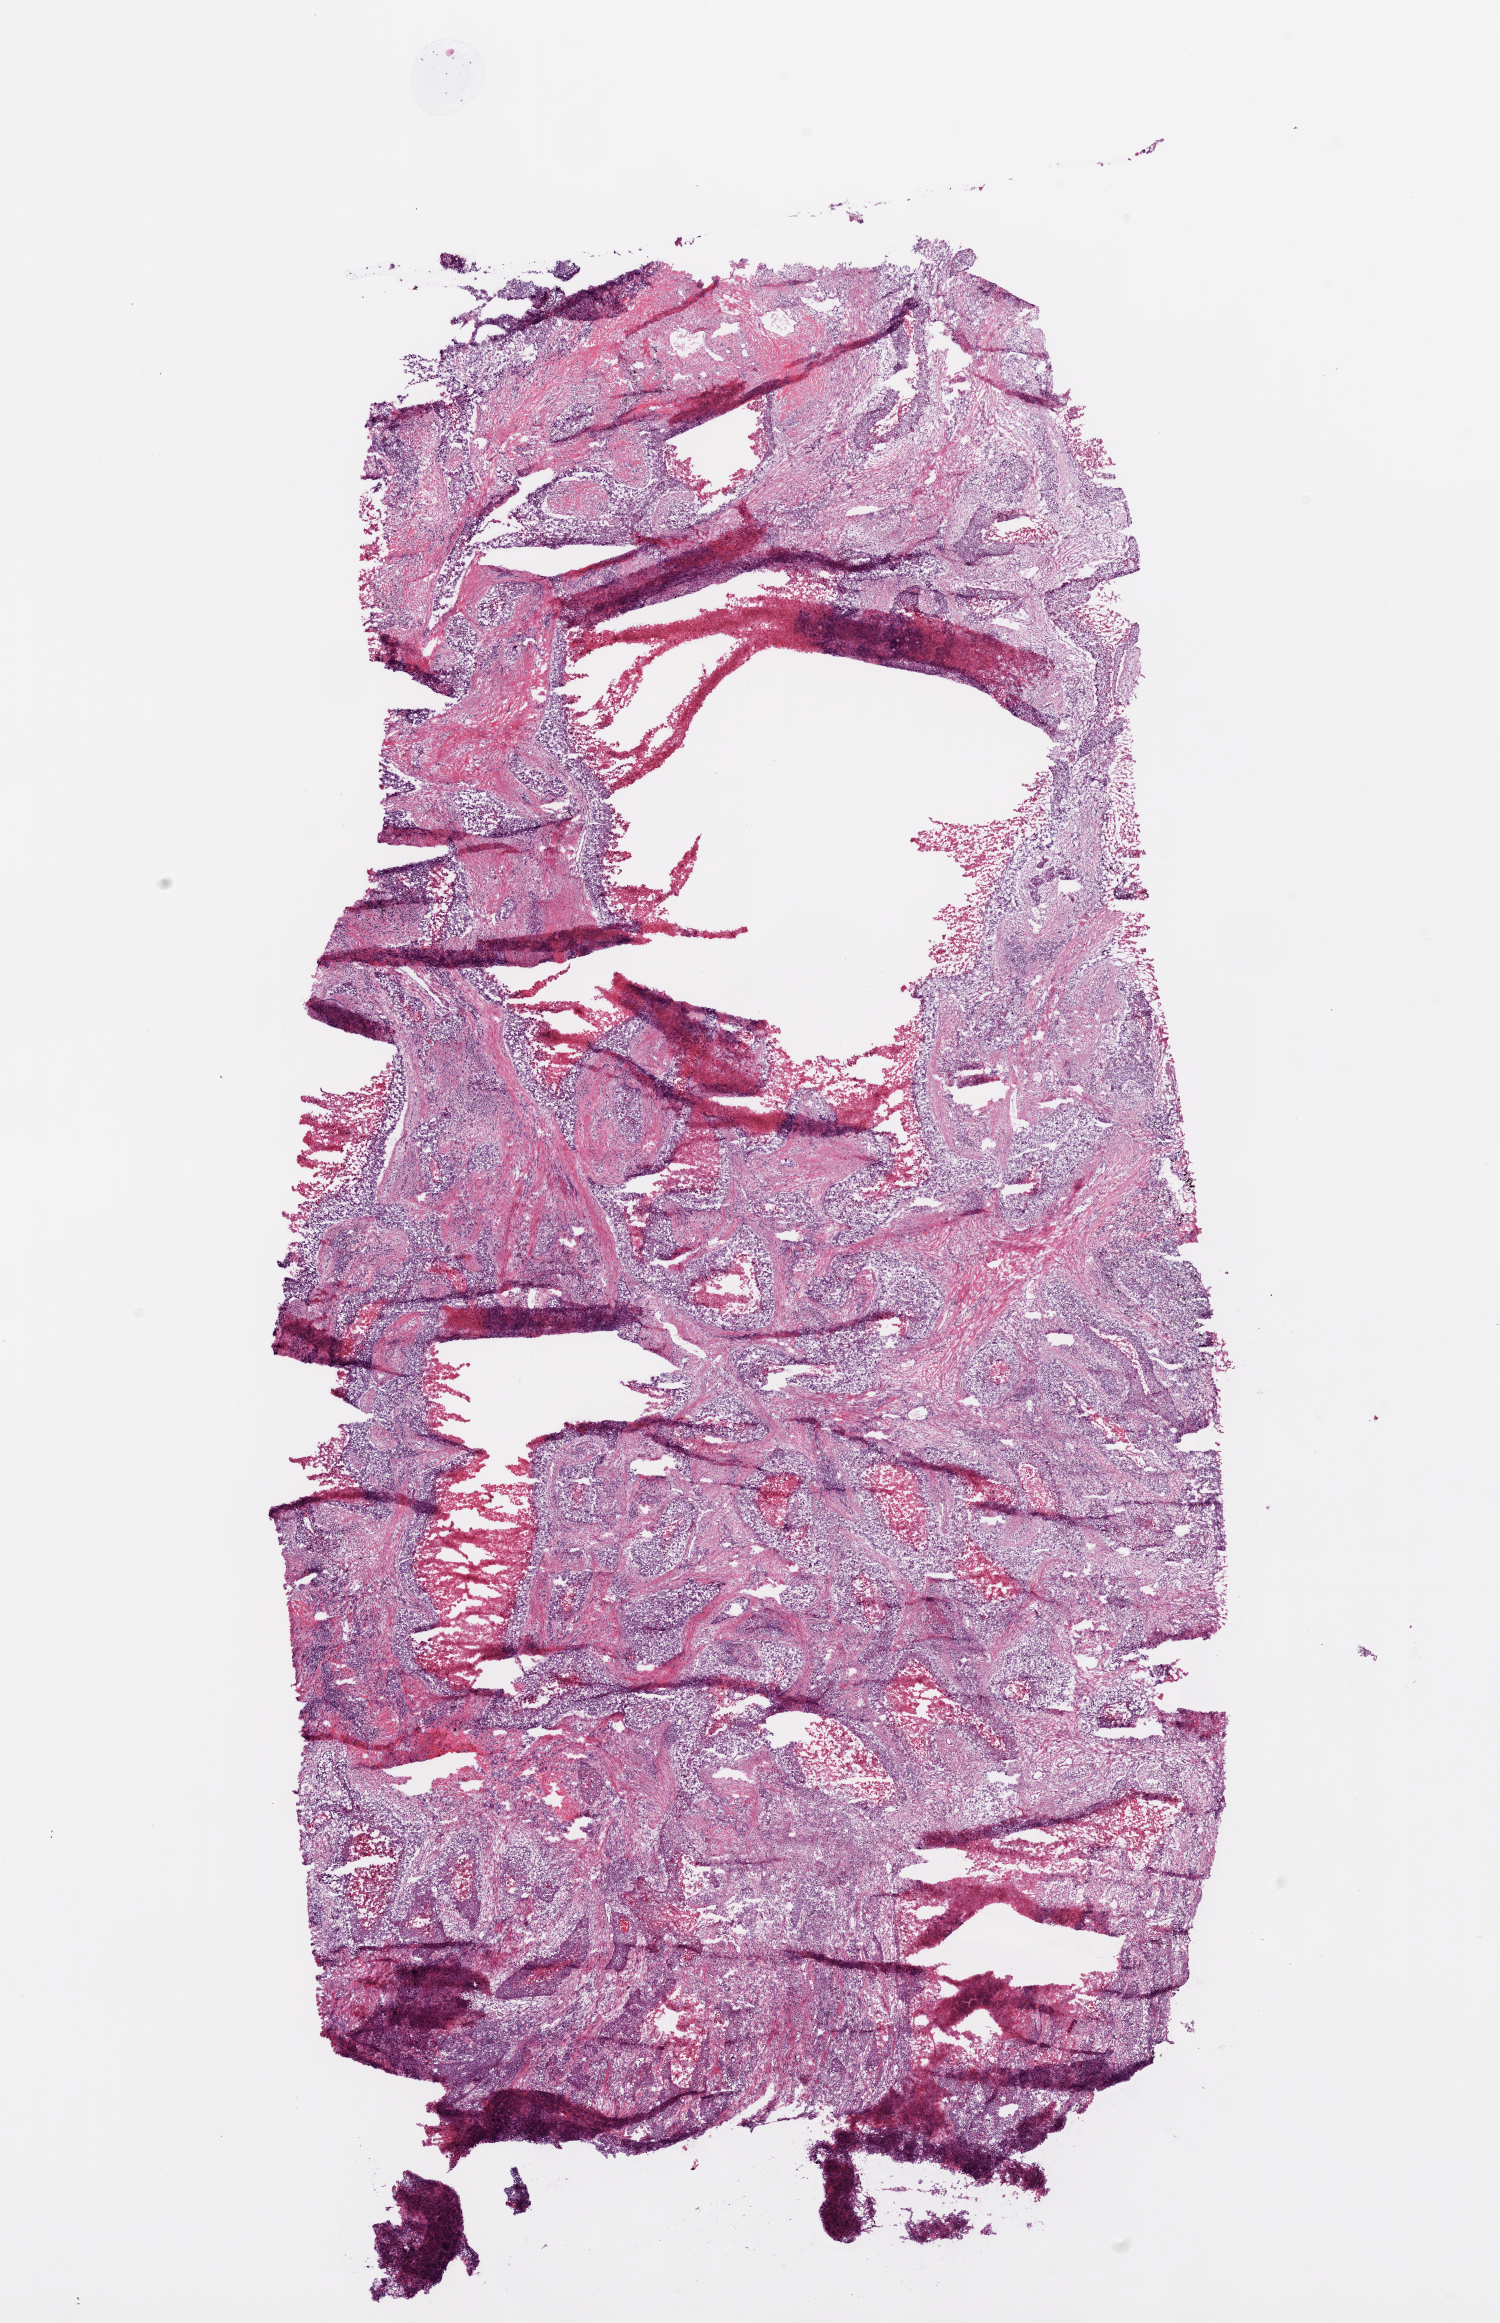
H&E-stained whole-slide image — shown as a low-resolution overview of the whole scanned area (about 12.0 x 18.6 mm), frozen section from the bottom of the tissue portion, lung, primary tumour sample. Male patient; age at initial diagnosis 76 years. Slide review estimates, as recorded: tumour cells 80%, tumour nuclei 85%, normal cells 0%, stromal cells 10%, necrosis 10%.
Laterality: right. AJCC pathologic stage: IIIB. Pathologic diagnosis: Squamous cell carcinoma, NOS.